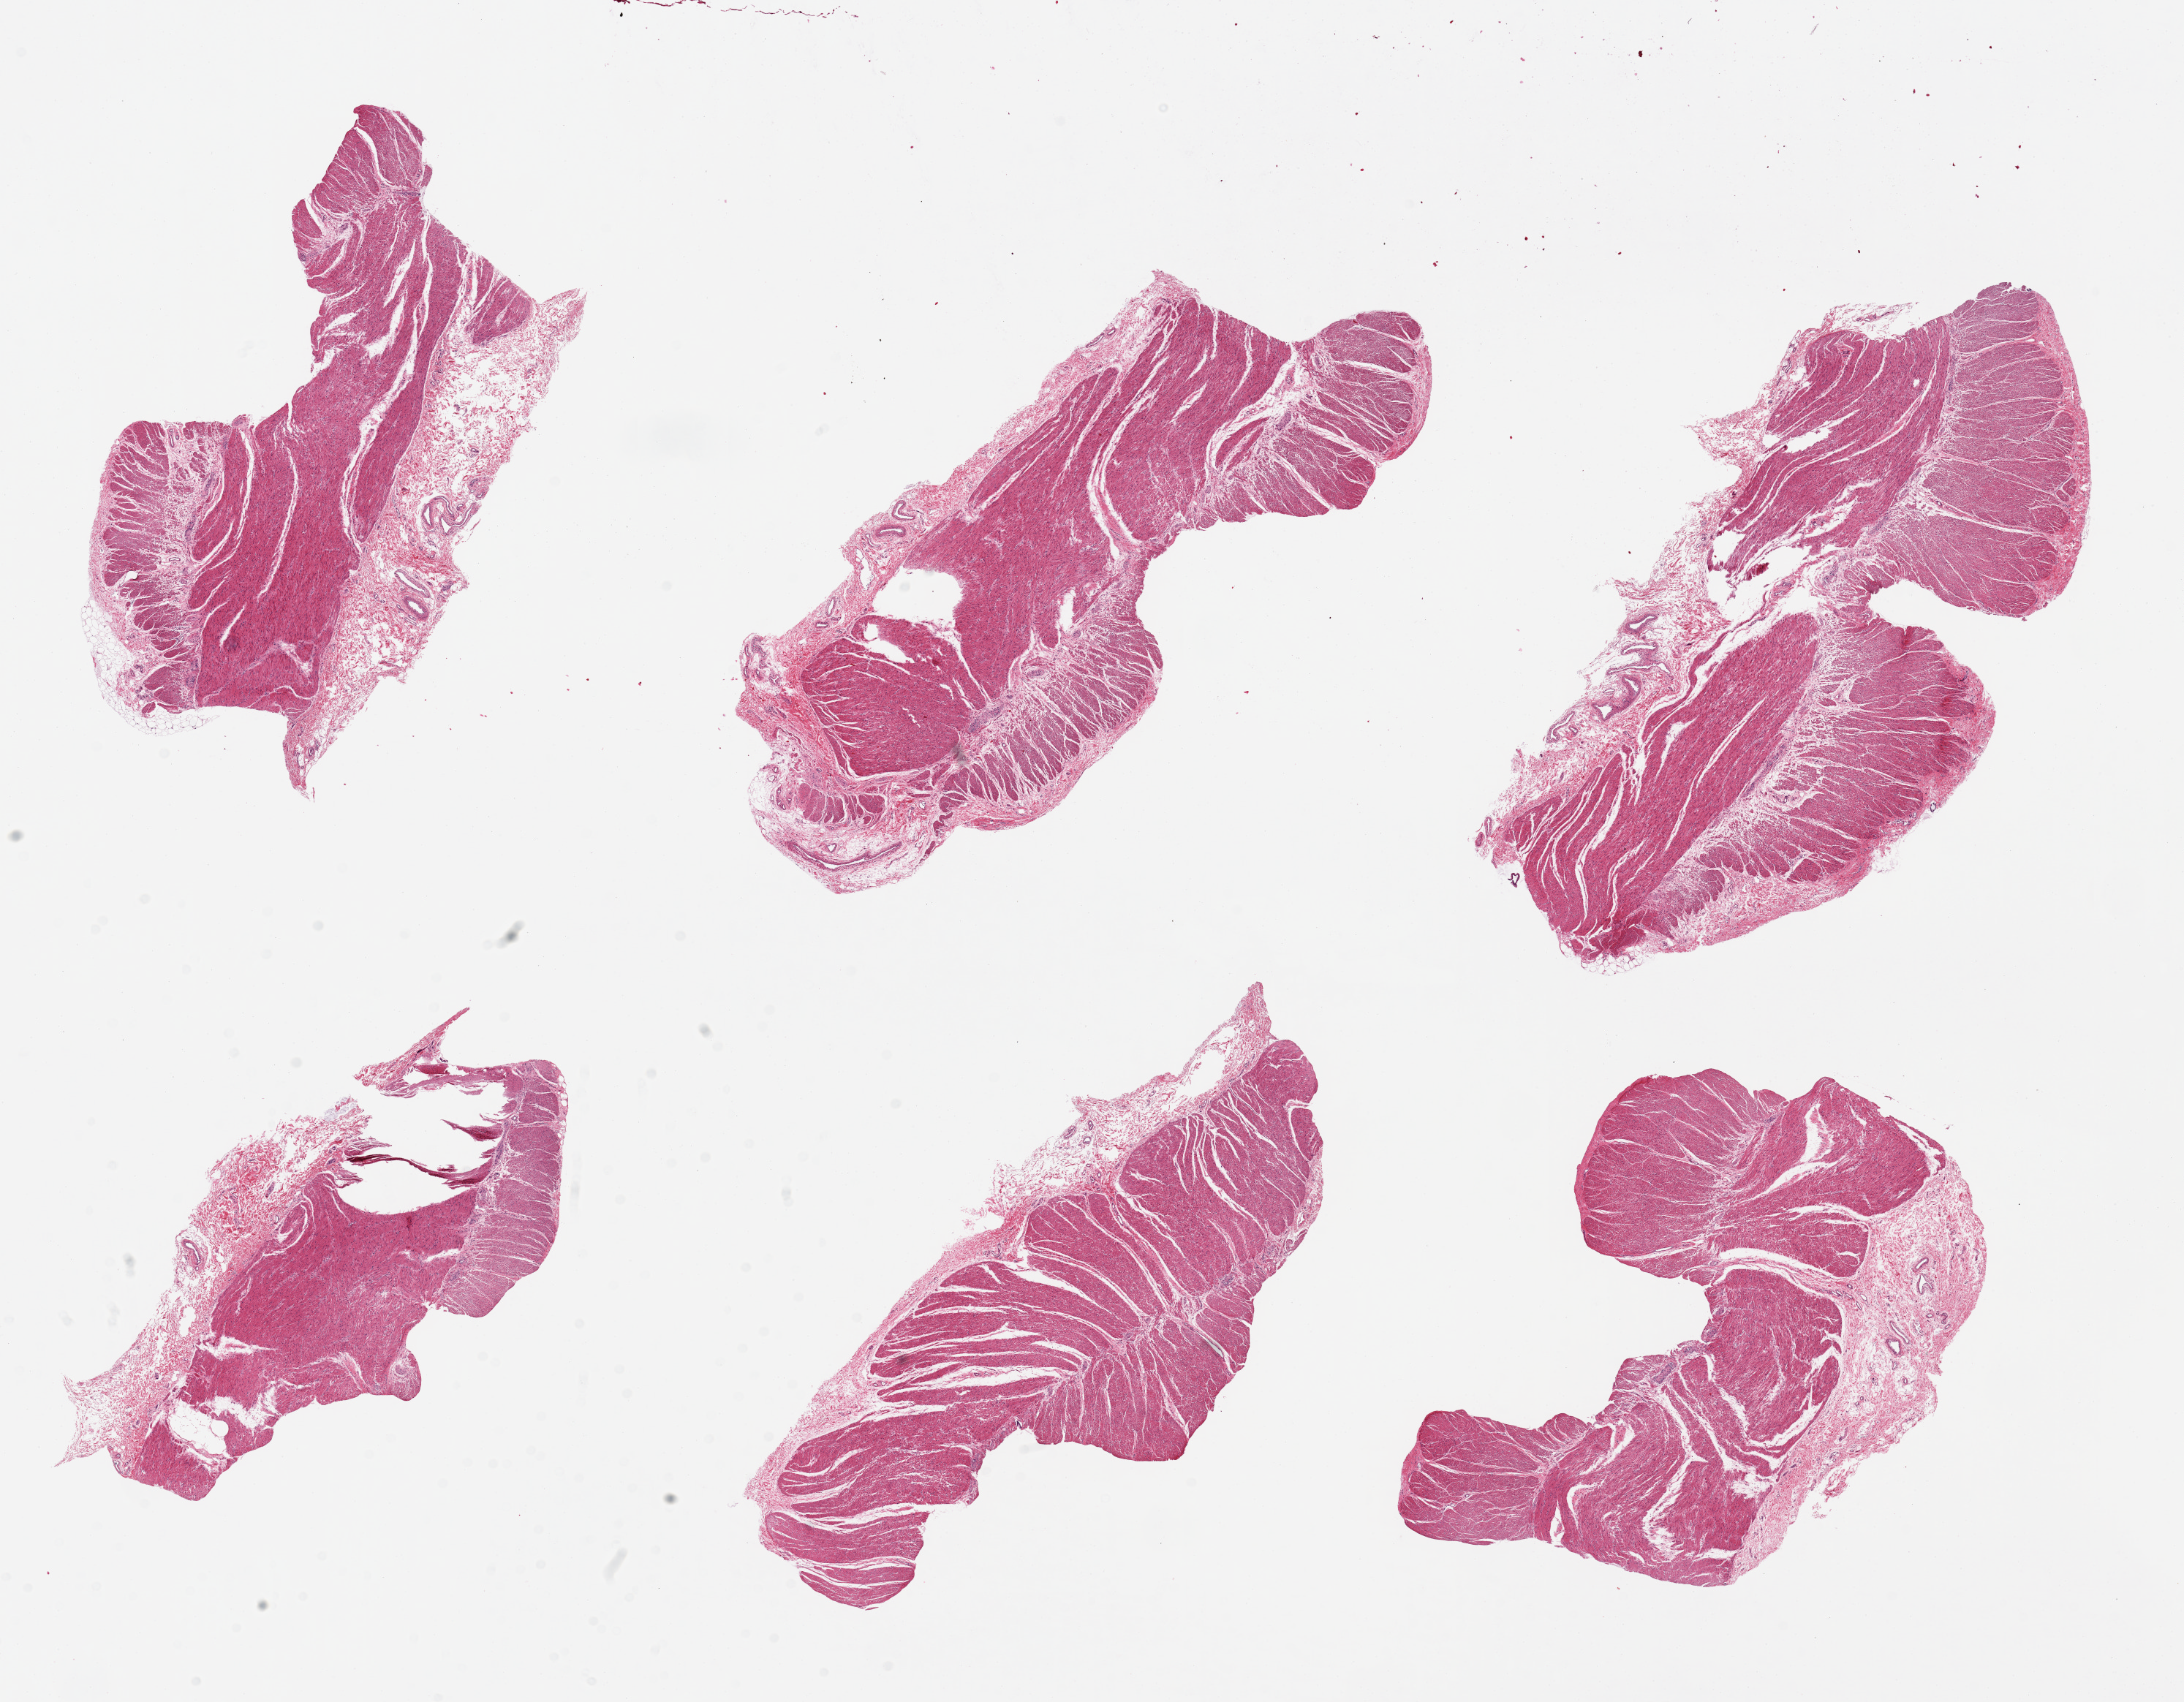
Digitized haematoxylin and eosin-stained section, brightfield — whole scanned area (about 23.6 x 18.4 mm, slide scanned at 20x) shown as a low-resolution overview, PAXgene-fixed, paraffin-embedded tissue, section of sigmoid colon (target tissue), donor tissue sample. Female donor.
- reviewer comment on this tissue sample: 6 pieces. up to 9x4mm; Well dissected: muscle mainly; no mucosa